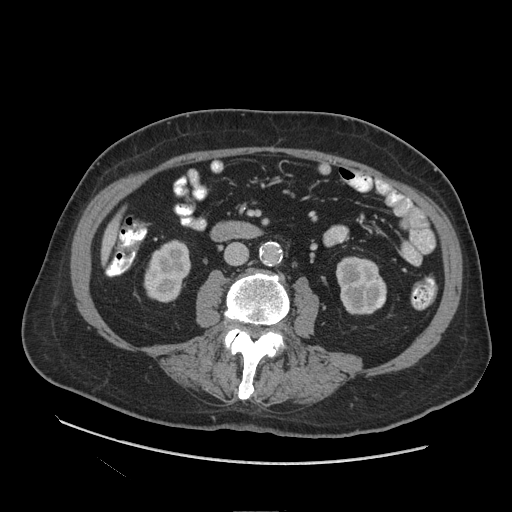
Contrast-enhanced abdominal CT (liver protocol), one axial slice; position 21 of 109 along the scan axis; reconstruction kernel STANDARD; soft-tissue window (W 400 / L 40 HU); 2.5 mm slice thickness; 512 × 512 image matrix, field of view 420 × 420 mm. Case-level facts recorded for this patient, not image findings: diagnosis: hepatocellular carcinoma (patient treated with transarterial chemoembolisation; whether this scan precedes or follows treatment is not stated here); TNM stage (as recorded): Stage-I; Child-Pugh class: A; tumour nodularity: uninodular.
Outlined on this slice (semi-automatically segmented with operator editing):
- liver parenchyma outside the tumour (the mass and vessels are separate outlines, so this box may not span the whole liver): bounding box <102,218,118,262> (left, top, right, bottom; pixels)